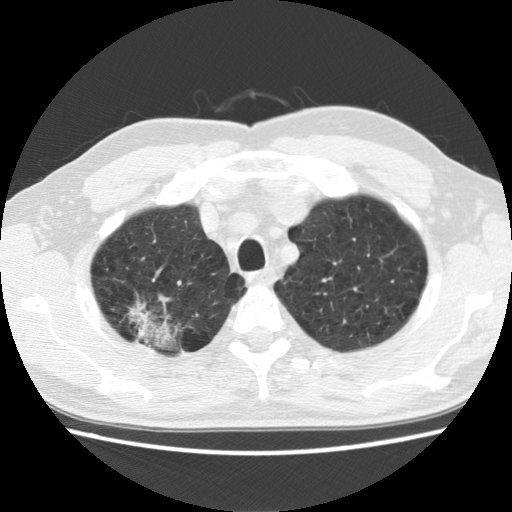
Axial slice from a low-dose chest CT screening exam. First (baseline) screen. Lung window (W 1500 / L -600 HU). 2.5 mm slice thickness. Standard (soft-tissue) reconstruction kernel (STANDARD). 120 kVp. Slice 27 of 142 in the series. 512 × 512 image matrix. Male, age 64 years at enrolment. Former smoker at enrolment.
Expert-annotated lung lesion, box from (x=109, y=290) to (x=197, y=363) px. Reader record for this screening exam (exam-level; its link to the box is not recorded): non-calcified nodule or mass ≥4 mm, right upper lobe, 39 × 31 mm, spiculated (stellate) margins, mixed attenuation. Official screen result: positive, change unspecified: nodule(s) >= 4 mm or enlarging nodule(s), mass(es), or other non-specific abnormalities suspicious for lung cancer. Later outcome: lung cancer diagnosed 74 days after this screen — adenocarcinoma, NOS, right upper lobe, moderately differentiated (G2), stage IB (AJCC 6th edition), 40 mm at pathology.